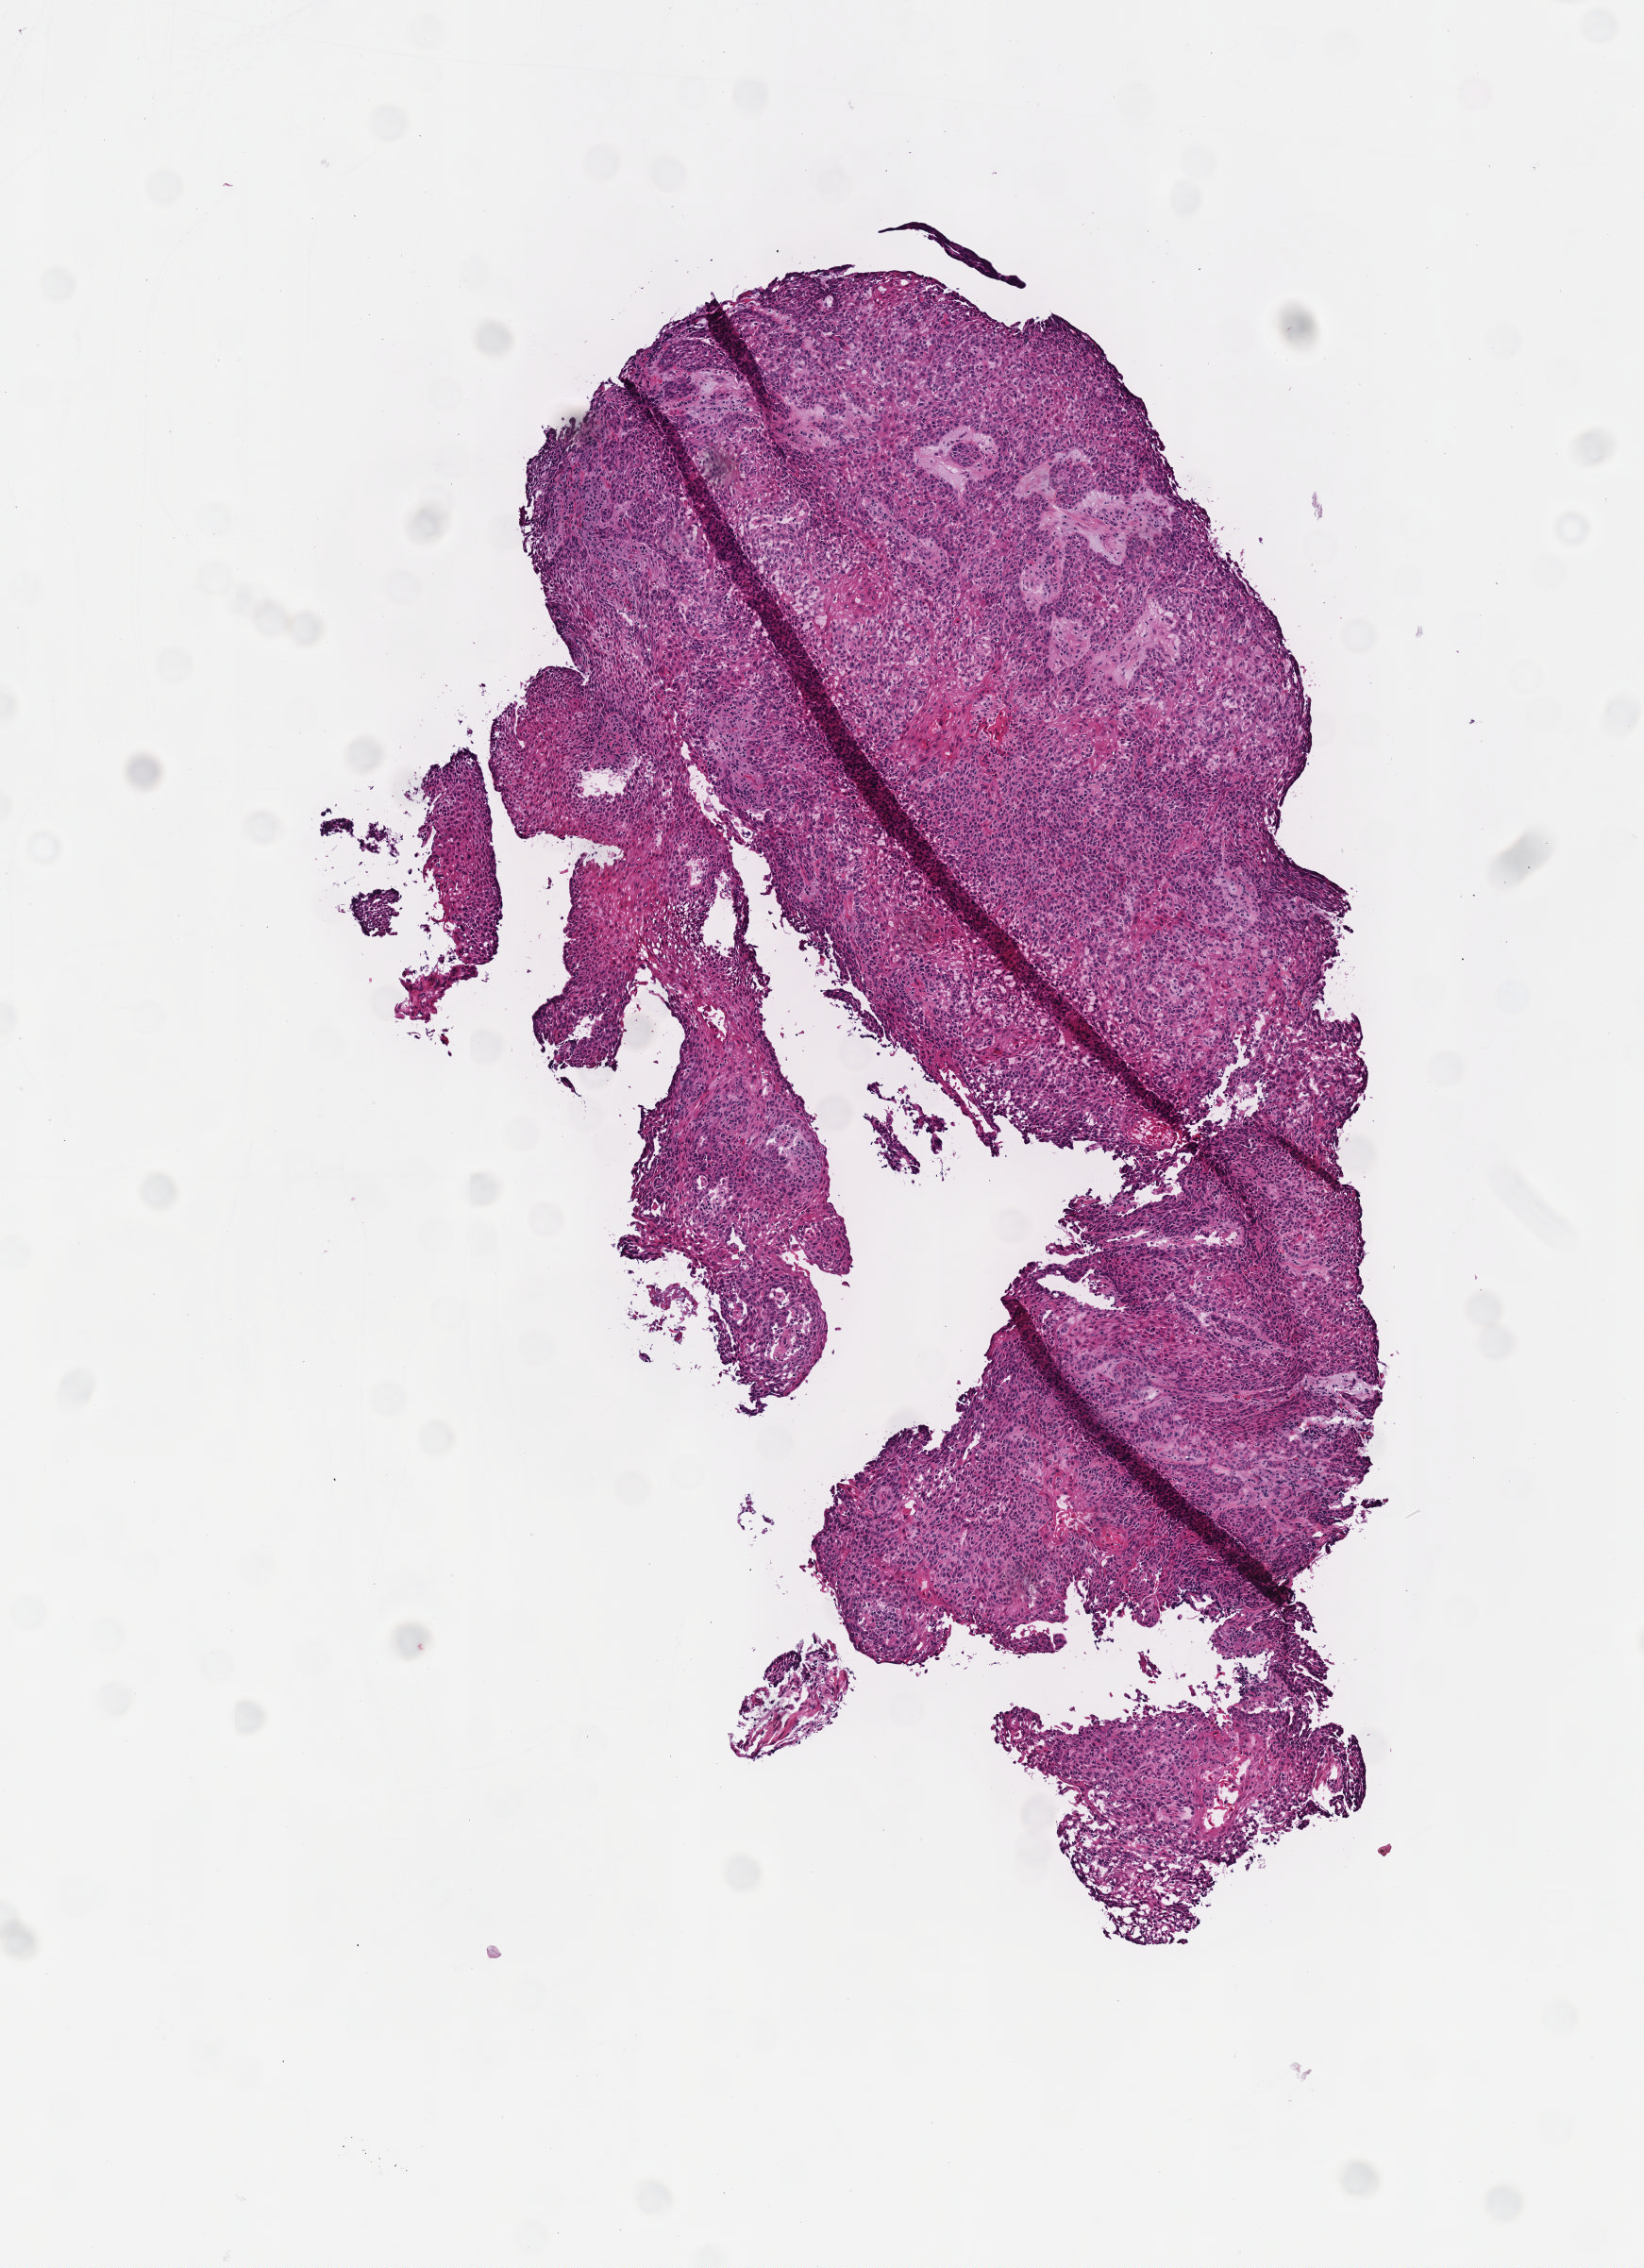
Digitized H&E tissue section (whole slide) — a low-resolution overview of the entire scanned area, about 3.5 x 4.9 mm (slide scanned at 40x), frozen section from the top of the tissue portion, esophagus, primary tumour sample. Male patient; age at initial diagnosis 67 years. Histologic grade: G3 (poorly differentiated). Composition of this section per pathologist review: tumour cells 80%, tumour nuclei 80%, normal cells 0%, stromal cells 20%, necrosis 0%. Inflammatory infiltration, as recorded: lymphocyte infiltration 40%, monocyte infiltration 20%, neutrophil infiltration 20%.
Histologic diagnosis: Squamous cell carcinoma, NOS. AJCC pathologic stage: IIB (7th edition).